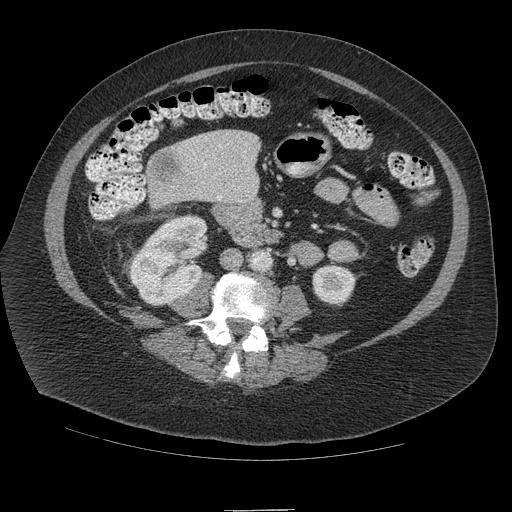
Contrast-enhanced abdominal CT (liver protocol), one axial slice. 140 kVp. Soft-tissue window (W 400 / L 40 HU). 512 × 512 image matrix, field of view 420 × 420 mm. Case-level facts recorded for this patient, not image findings: diagnosis: hepatocellular carcinoma (patient treated with transarterial chemoembolisation; whether this scan precedes or follows treatment is not stated here); TNM stage (as recorded): Stage-IVB; Child-Pugh class: A; tumour differentiation: poorly differentiated.
Annotated regions visible in this slice (semi-automatically segmented with operator editing):
- liver parenchyma outside the tumour (the mass and vessels are separate outlines, so this box may not span the whole liver): box from (x=186, y=130) to (x=260, y=197) px
- mass: (x=144, y=148)–(x=183, y=191)
- liver vessels: (x=190, y=137)–(x=249, y=171)